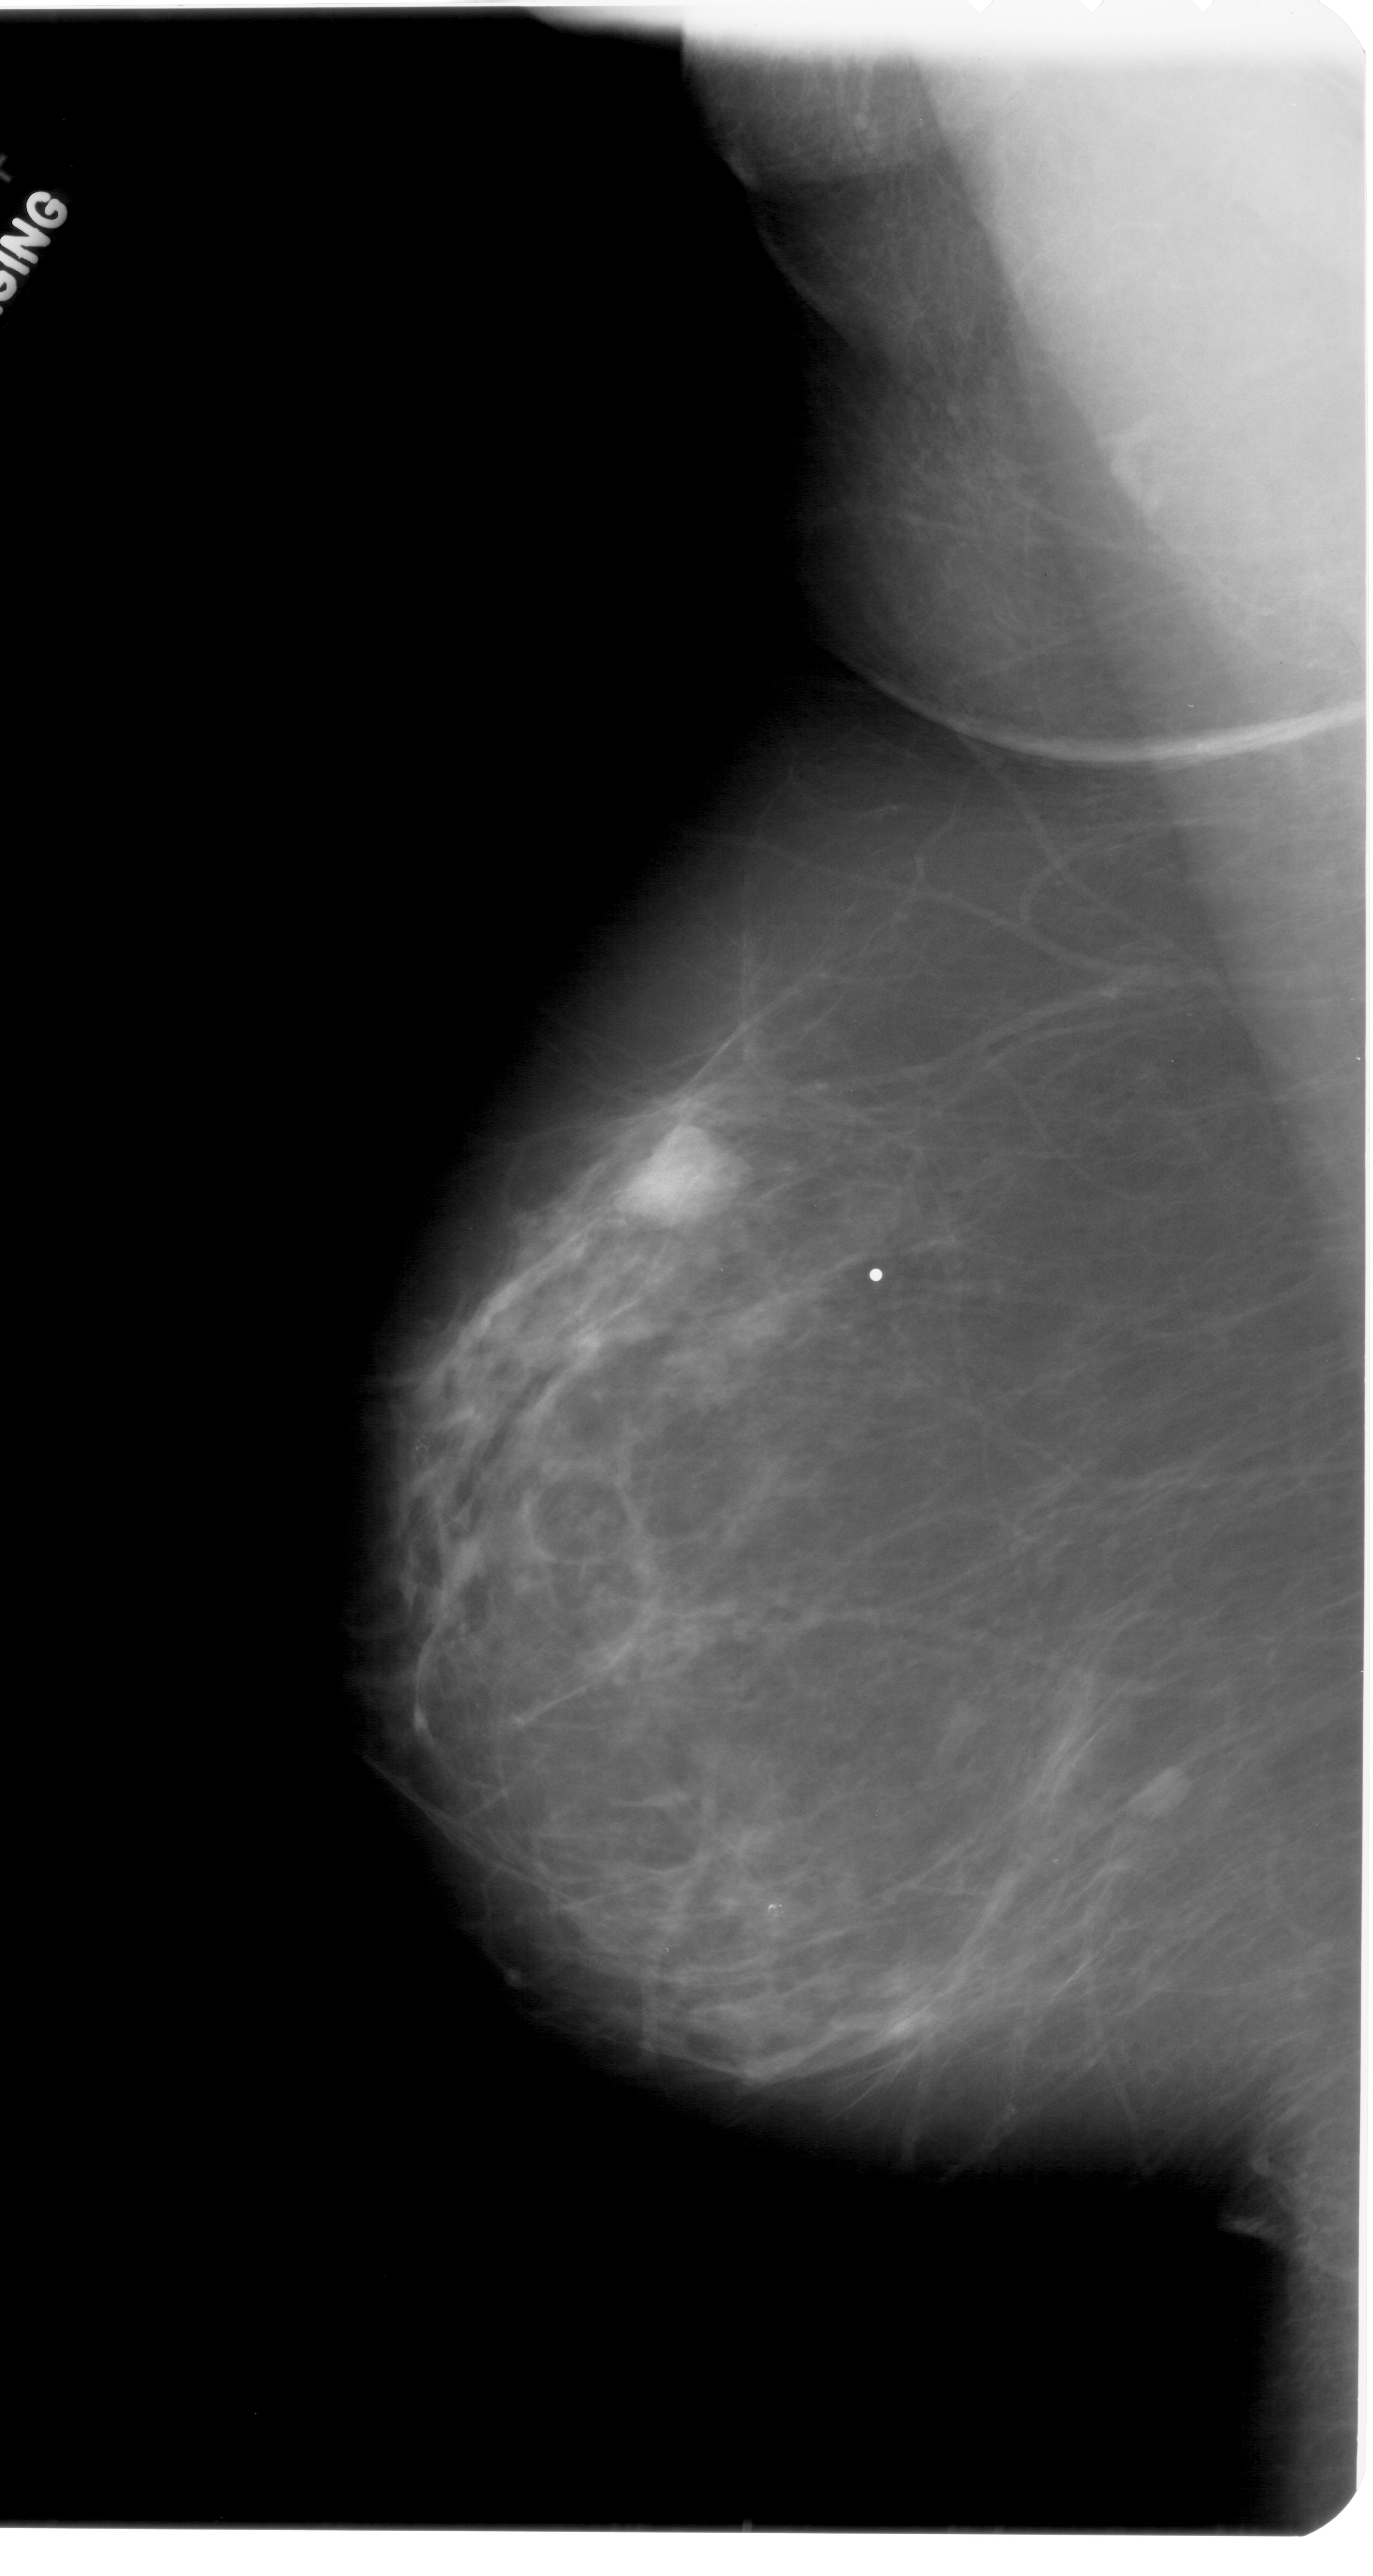
Mammogram (digitized film). Left breast. Mediolateral oblique (MLO) view. Breast composition: scattered fibroglandular densities (BI-RADS density category 2 of 4). 1373 × 2576 image matrix.
Expert-marked regions of interest on this image (one box per marked abnormality):
- mass, shape lobulated, margins circumscribed; BI-RADS assessment category 4; pathology (as recorded): benign: bounding box [x1, y1, x2, y2] px = [621, 1129, 735, 1228]